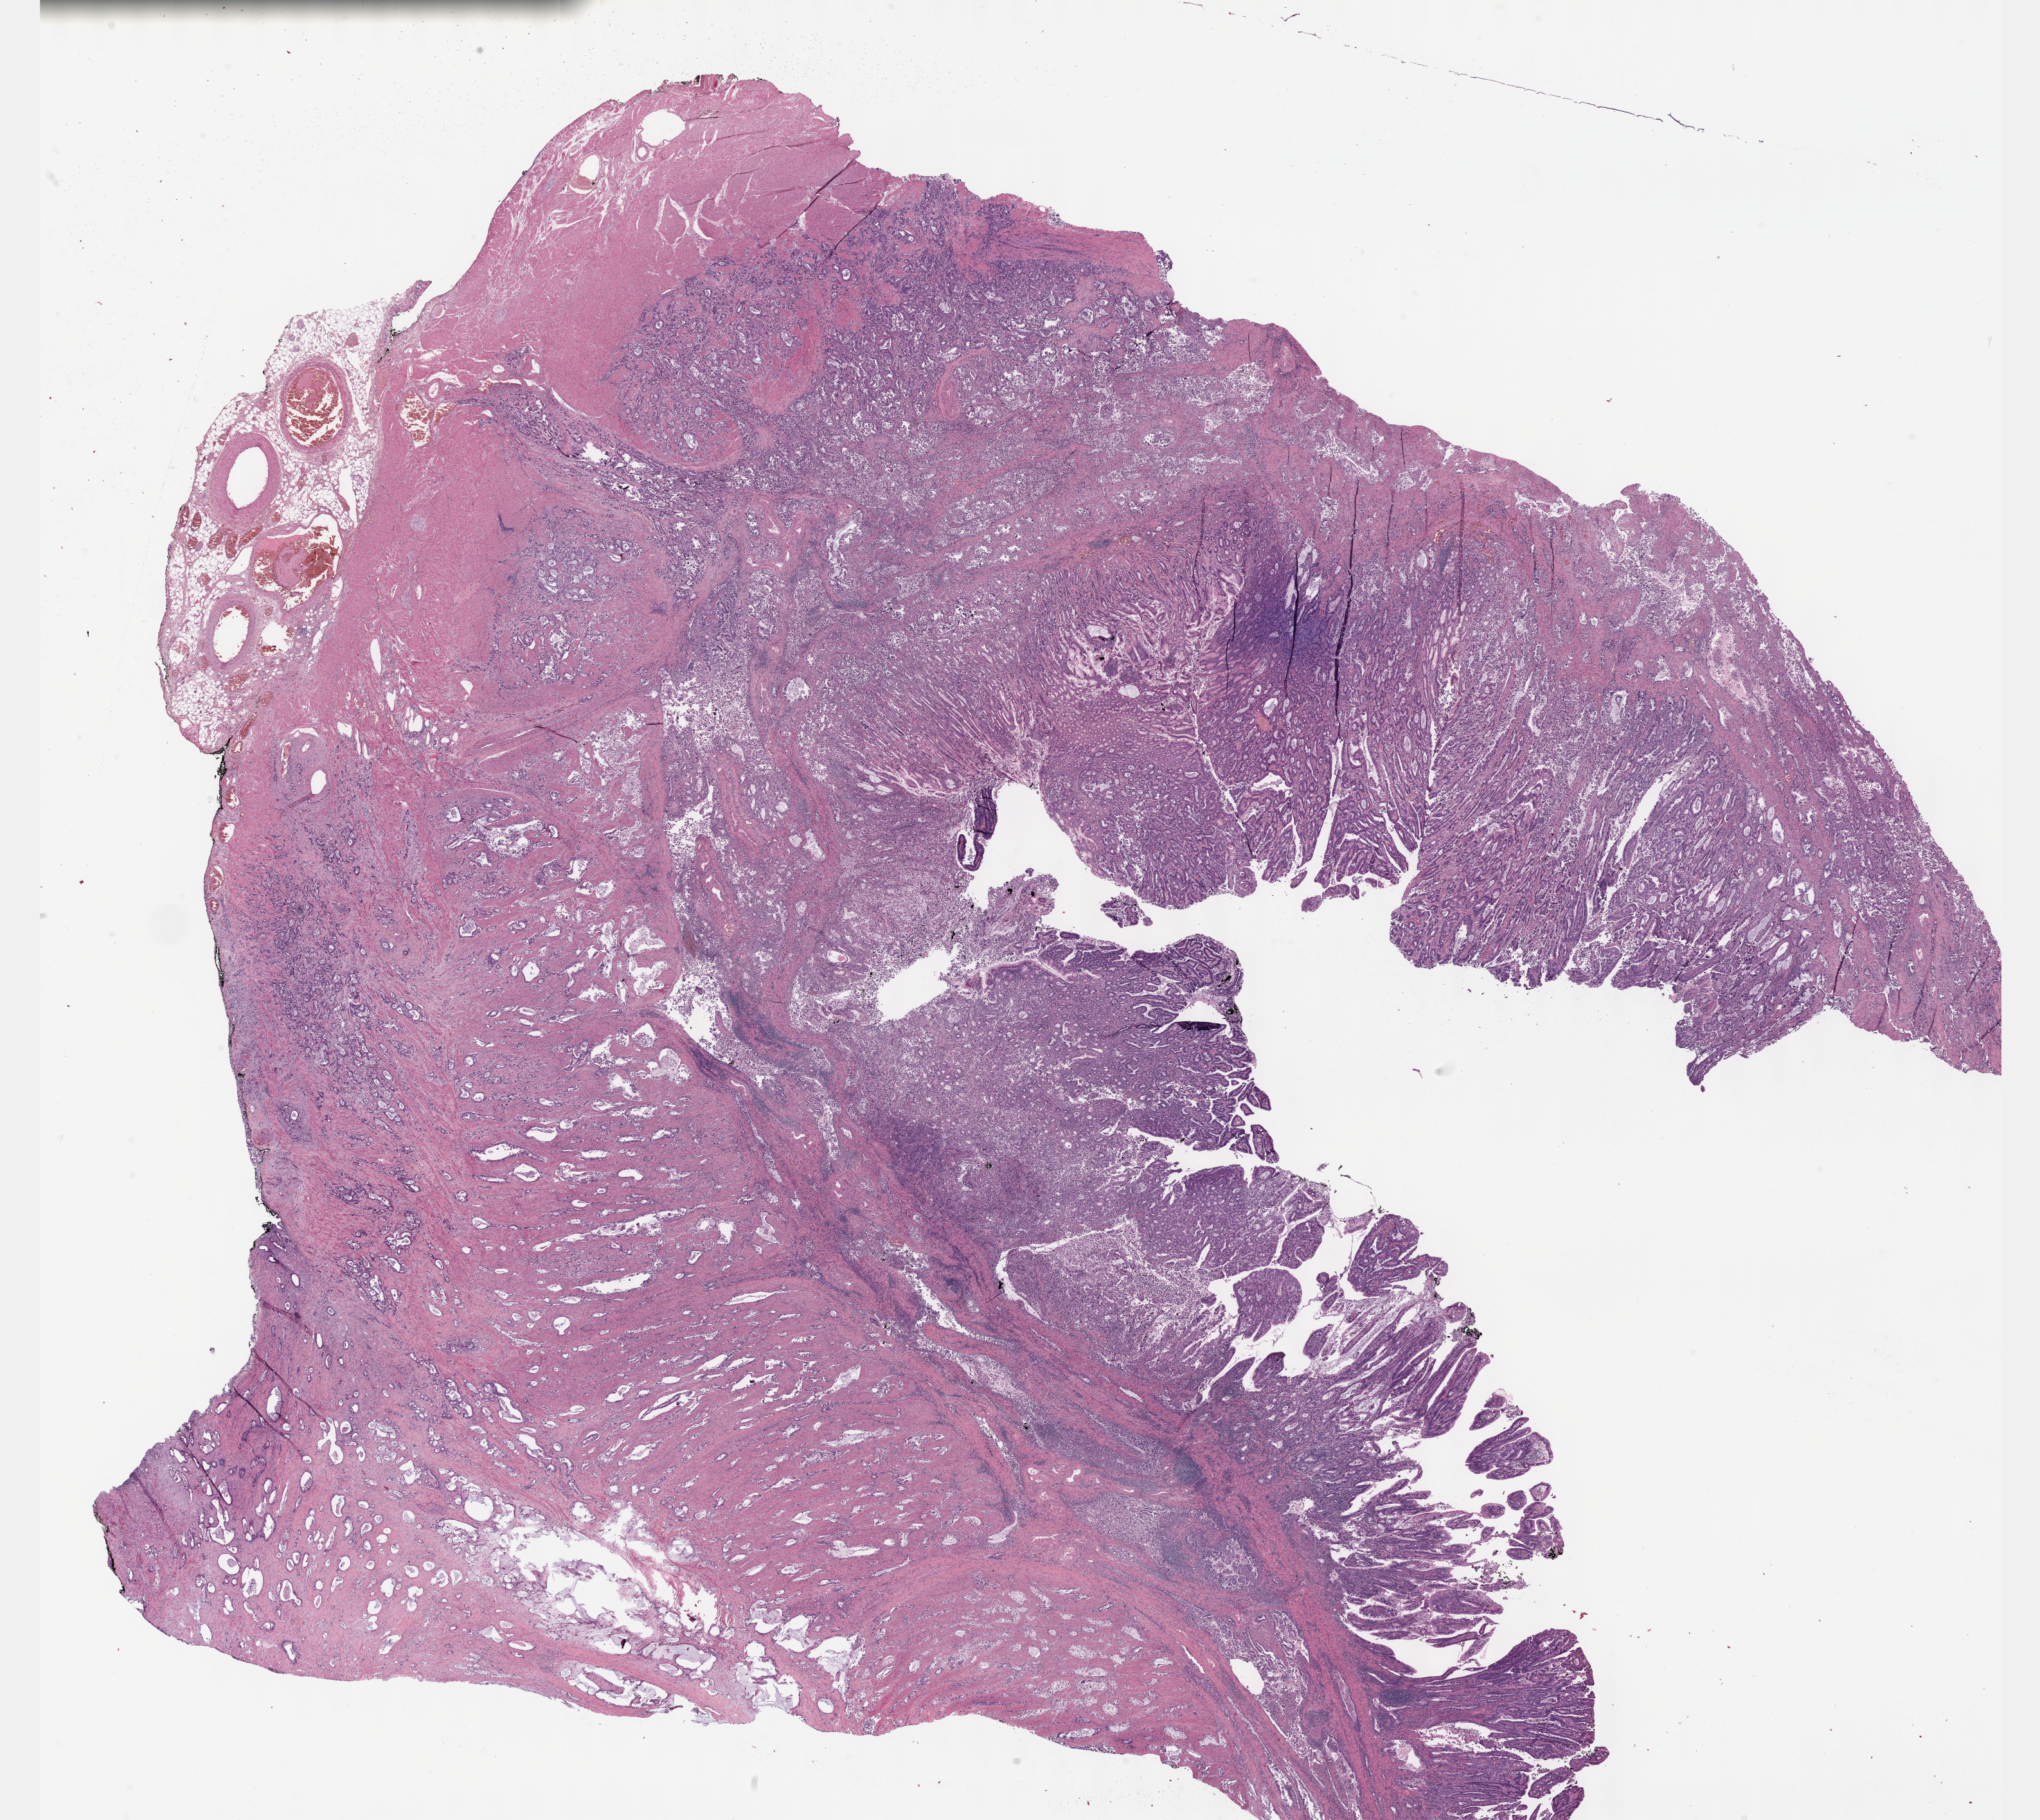
Whole-slide histology image, H&E-stained, shown as a low-resolution overview of the whole scanned area (about 25.7 x 22.9 mm, slide scanned at 40x), FFPE section, primary tumour sample from the stomach. Male, age 66 years at initial diagnosis. Histologic grade: G2 (moderately differentiated).
• TNM: T3 N2 M0
• AJCC pathologic stage: IIIA
• lymph nodes positive (case pathology): 6 of 6 examined
• pathologic diagnosis: Tubular adenocarcinoma (gastric antrum)